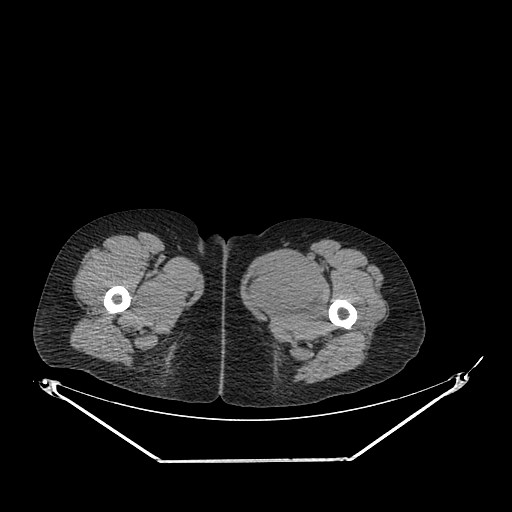
CT of an extremity soft-tissue mass (from a PET/CT study), one axial slice; position 250 of 267 along the scan axis; reconstruction kernel SOFT; soft-tissue window (W 400 / L 40 HU); 3.75 mm slice thickness; 512 × 512 image matrix, field of view 500 × 500 mm. Female patient. From the clinical record (not read from this slice): histological type: pleiomorphic leiomyosarcoma; grade: intermediate; site of the primary tumour: left thigh.
Outlined on this slice (expert contour drawn on MRI and transferred to this co-registered scan by the dataset authors):
- gross tumour volume including surrounding oedema: box from (x=247, y=253) to (x=323, y=318) px
- gross tumour volume (mass): (x=247, y=253)–(x=323, y=318)